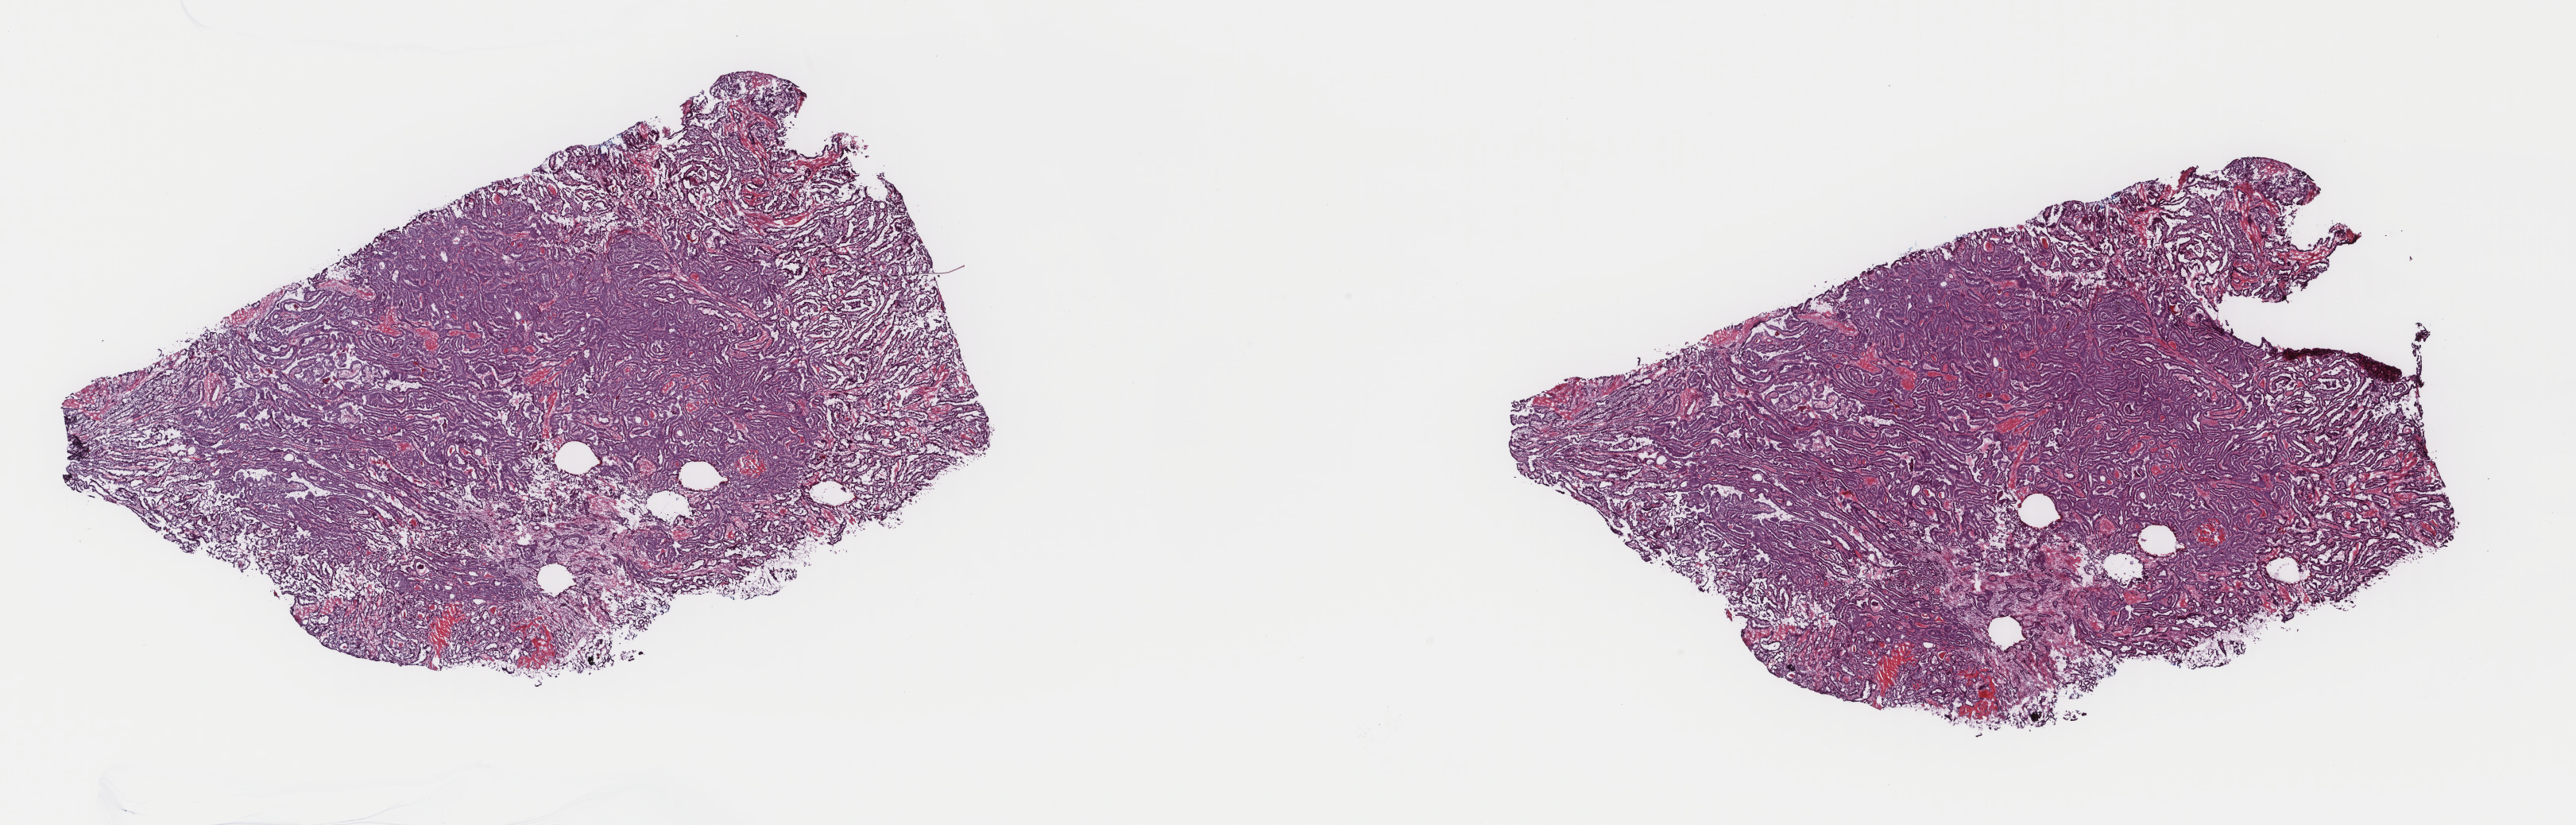
Whole-slide histology image, H&E, a low-resolution overview of the entire scanned area, about 25.7 x 8.2 mm (slide scanned at 40x). Frozen section from the top of the tissue portion. Sample: primary tumour, thyroid. Female patient; age at initial diagnosis 62 years. Composition of this section per pathologist review: tumour cells 100%, tumour nuclei 90%, normal cells 0%, stromal cells 0%, necrosis 0%. Infiltration values recorded for this section: lymphocyte infiltration 1%, monocyte infiltration 0%, neutrophil infiltration 0%.
AJCC pathologic stage: III (7th edition). Pathologic diagnosis: Papillary adenocarcinoma, NOS (thyroid gland).